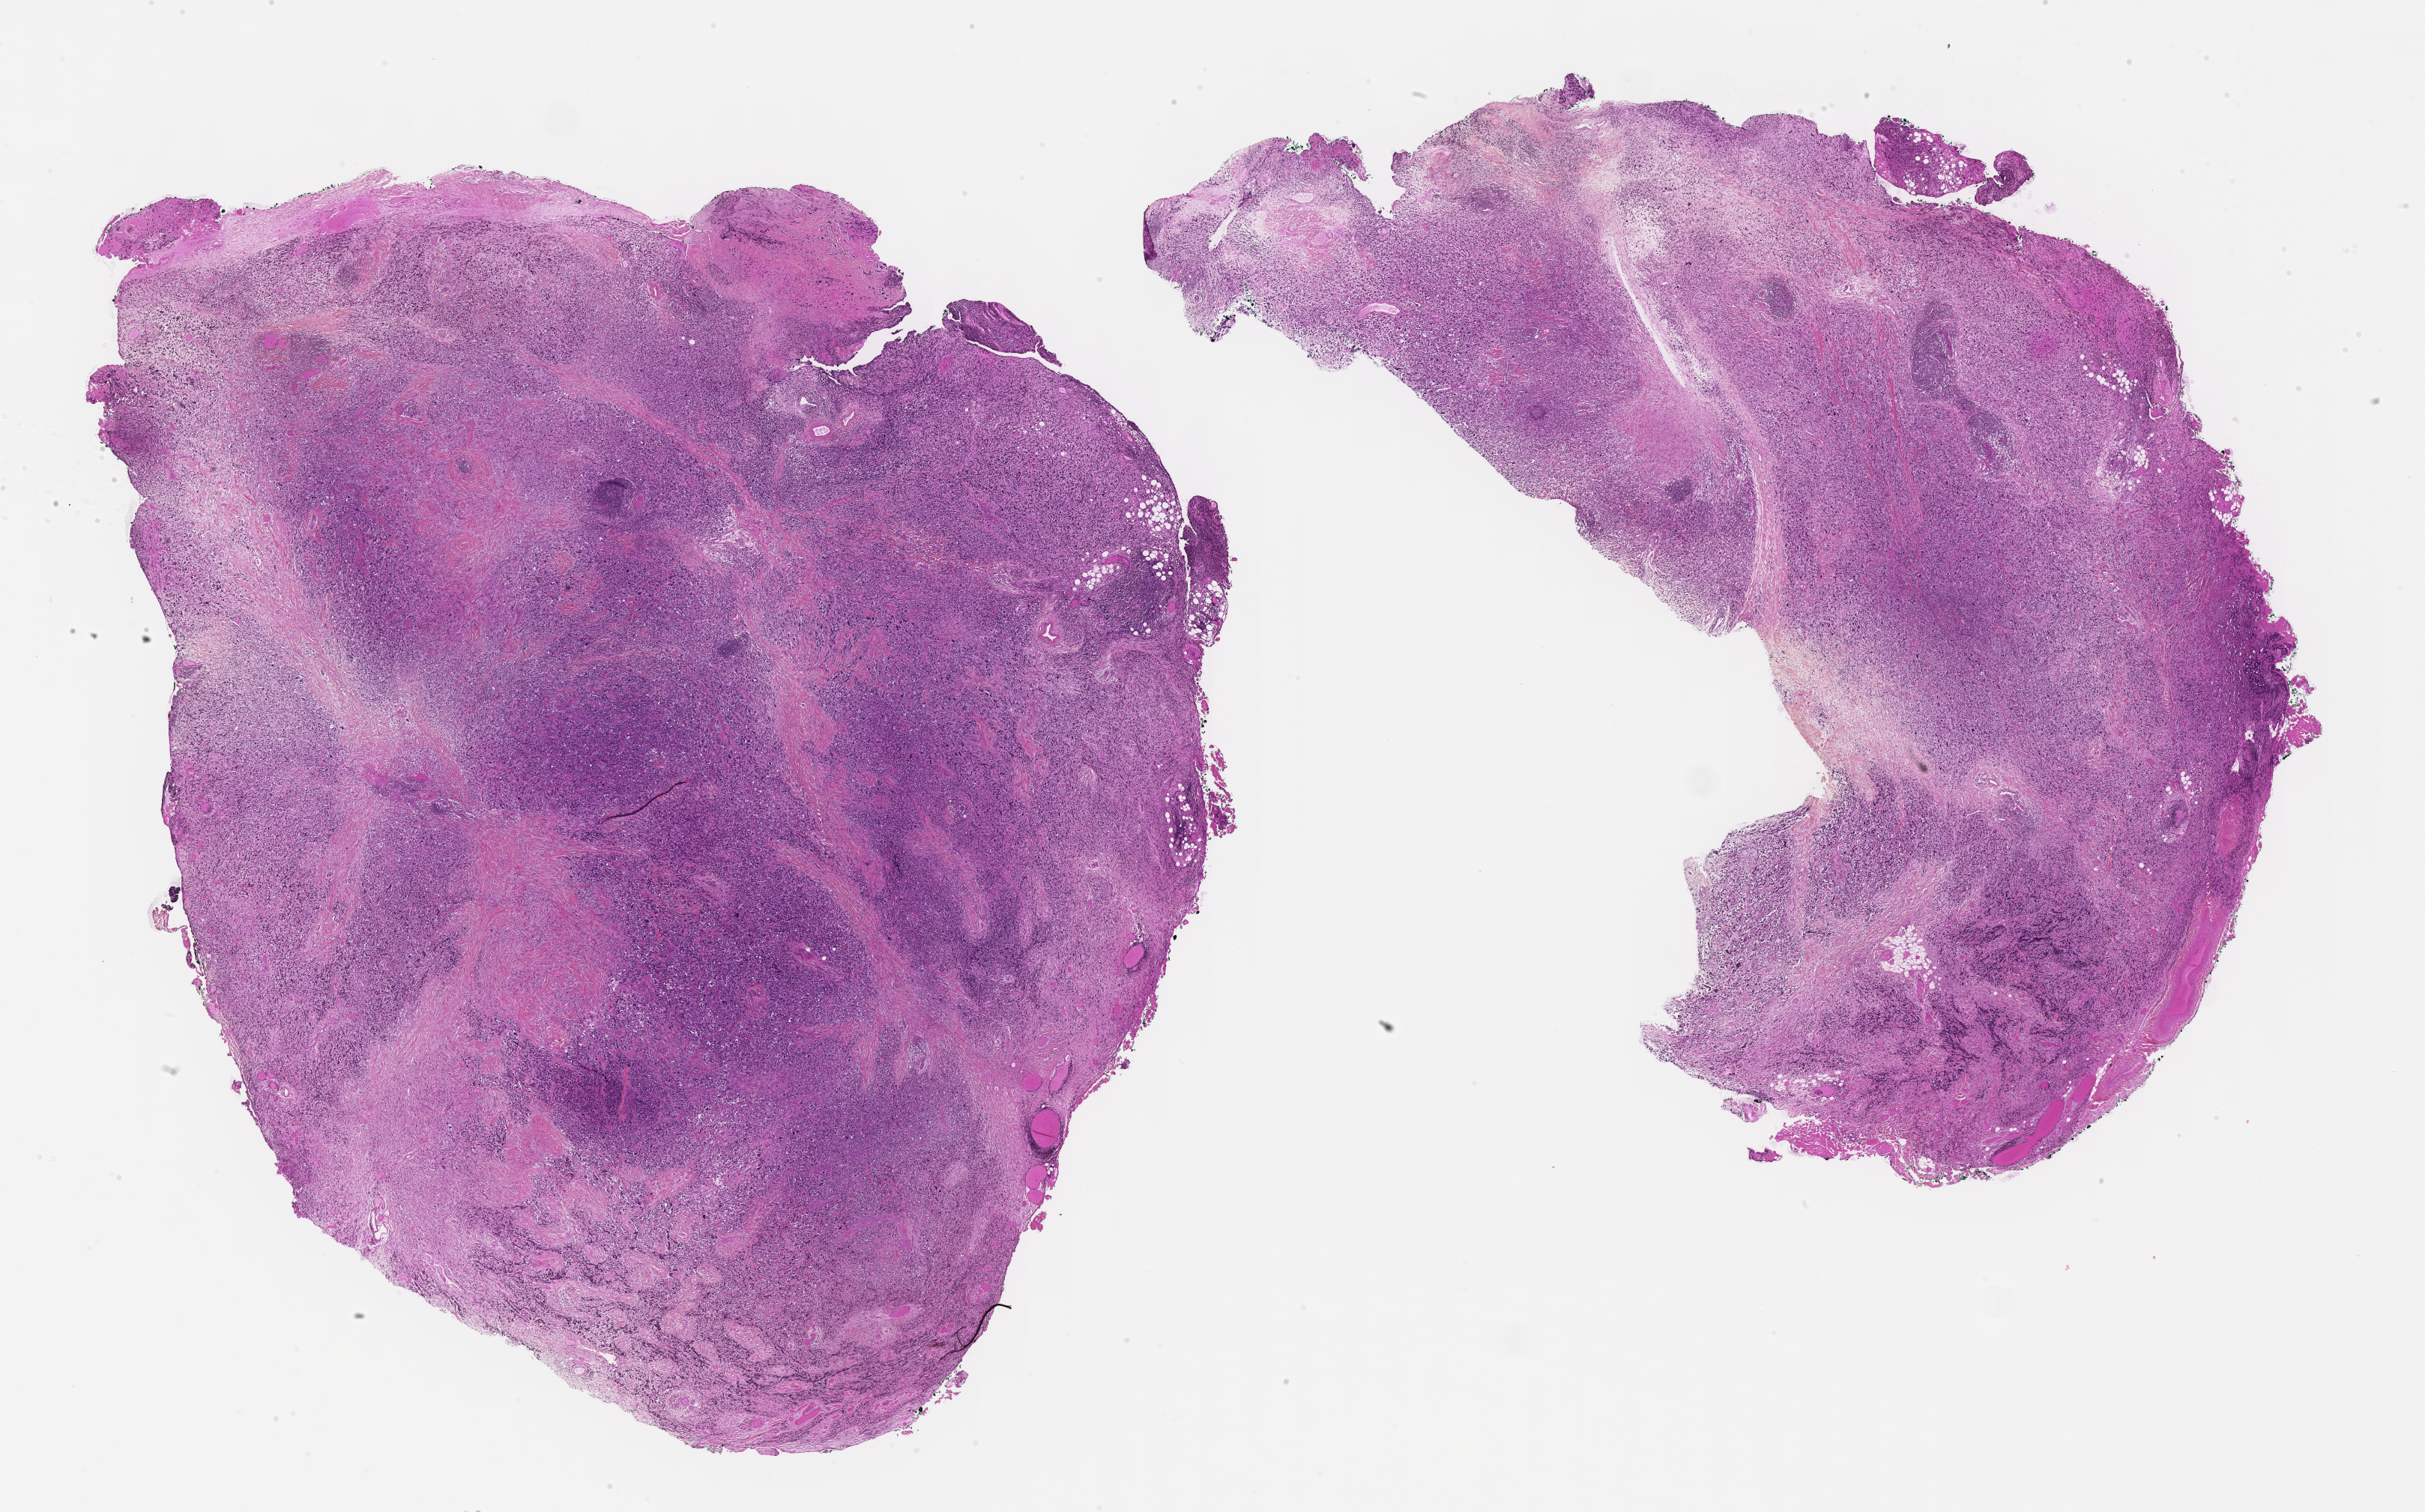
Digitized hematoxylin and eosin (H&E)-stained section of tumor tissue, whole scanned area (about 26.2 x 16.3 mm) shown as a low-resolution overview, formalin-fixed, paraffin-embedded (FFPE) tissue, sample anatomic site: nasal cavity-supra. Patient: male, age 4.2 years at diagnosis.
* stage (as recorded): 1
* diagnosis: rhabdomyosarcoma; histological classification: embryonal rhabdomyosarcoma
* primary site (case record): paranasal sinus (PM)
* metastatic status at presentation (as recorded): non-metastatic (confirmed)